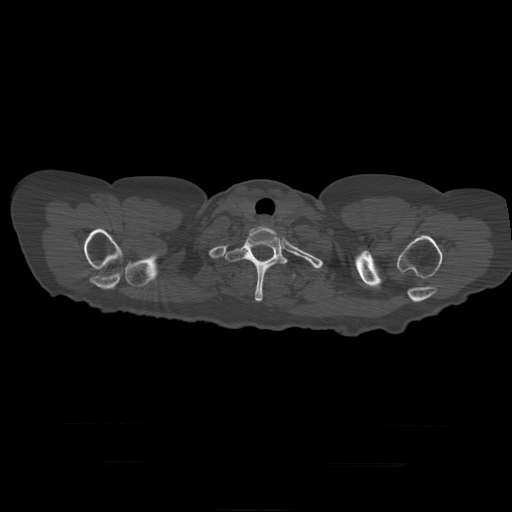
CT including the spine, one axial slice. Slice 378 of 399 in the series (ordered by position). Reconstruction kernel STANDARD. 120 kVp. Bone window (W 1800 / L 400 HU). 512 × 512 image matrix. Patient age 41 years. From the clinical record (not read from this slice): primary cancer: breast.
Annotated regions visible in this slice (semi-automatically segmented with operator editing):
- T1 vertebra: bounding box <249,226,278,241> (left, top, right, bottom; pixels)
- T2 vertebra: <225,236,288,302>
- T3 vertebra: <293,275,296,277>